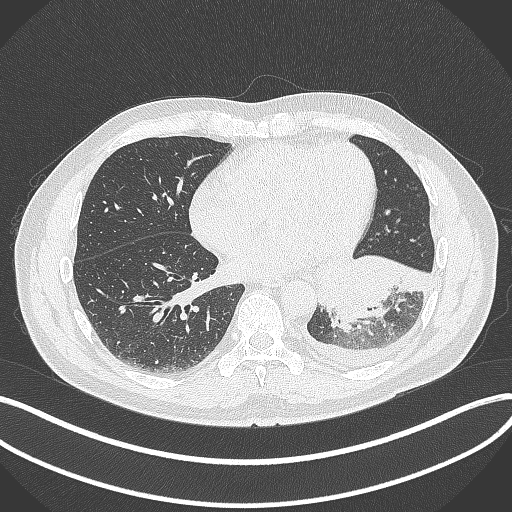
Chest CT, one axial slice; position 132 of 342 along the scan axis; reconstruction kernel B70f; lung window (W 1500 / L -600 HU); 1 mm slice thickness; 512 × 512 image matrix, field of view 400 × 400 mm. Patient: male, 58 years. Case-level facts recorded for this patient, not image findings: clinical TNM (as recorded): T3 N1 M1b; histopathological grade: G3.
Structures marked on this image (rectangle marked by the reading radiologist):
- lung tumour (recorded histology: small cell carcinoma): bounding box (x1, y1, x2, y2) in pixels: (313, 252, 429, 335)